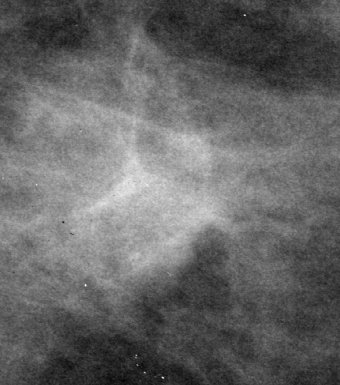
Region of interest cut from a scanned film mammogram (one marked finding); left breast; CC view.
Finding: mass, shape lobulated, margins ill defined; BI-RADS assessment category 5; pathology (as recorded): malignant.